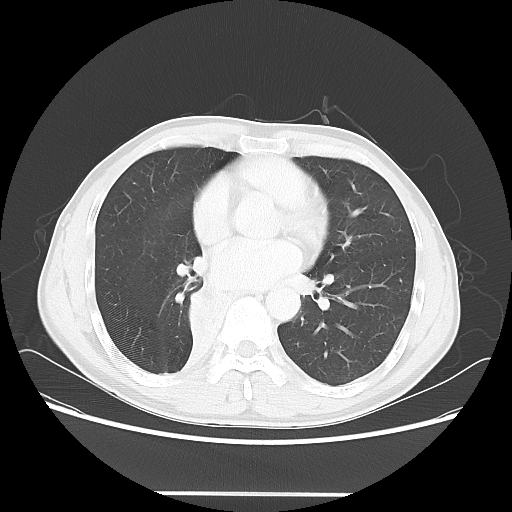
Chest CT, one axial slice; slice 29 of 62 in the series (ordered by position); reconstruction kernel LUNG; 120 kVp; lung window (W 1500 / L -600 HU); 512 × 512 image matrix, field of view 393 × 393 mm. Male patient, age 47 years. From the clinical record (not read from this slice): clinical TNM (as recorded): T2 N0 M0.
Annotated regions visible in this slice (bounding box drawn by a radiologist):
- lung tumour (recorded histology: squamous cell carcinoma): bounding box [x1, y1, x2, y2] px = [182, 283, 232, 350]